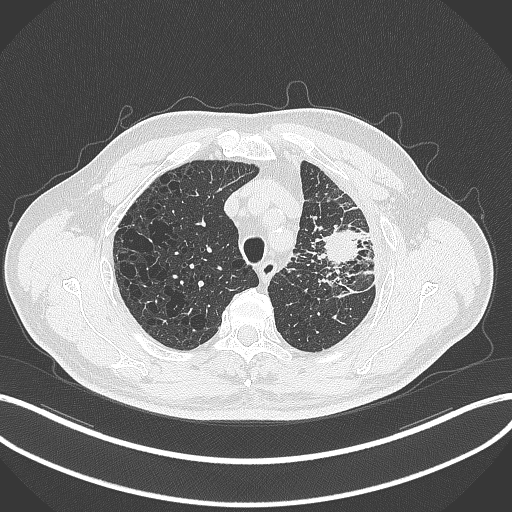
Chest CT, one axial slice; position 255 of 297 along the scan axis; reconstruction kernel B70f; 120 kVp; lung window (W 1500 / L -600 HU); 1 mm slice thickness; 512 × 512 image matrix. Male patient, age 68 years. Case-level facts recorded for this patient, not image findings: clinical TNM (as recorded): T3 N3 M1.
Annotated regions visible in this slice (rectangle marked by the reading radiologist):
- lung tumour (recorded histology: adenocarcinoma): bounding box [x1, y1, x2, y2] px = [316, 222, 364, 270]